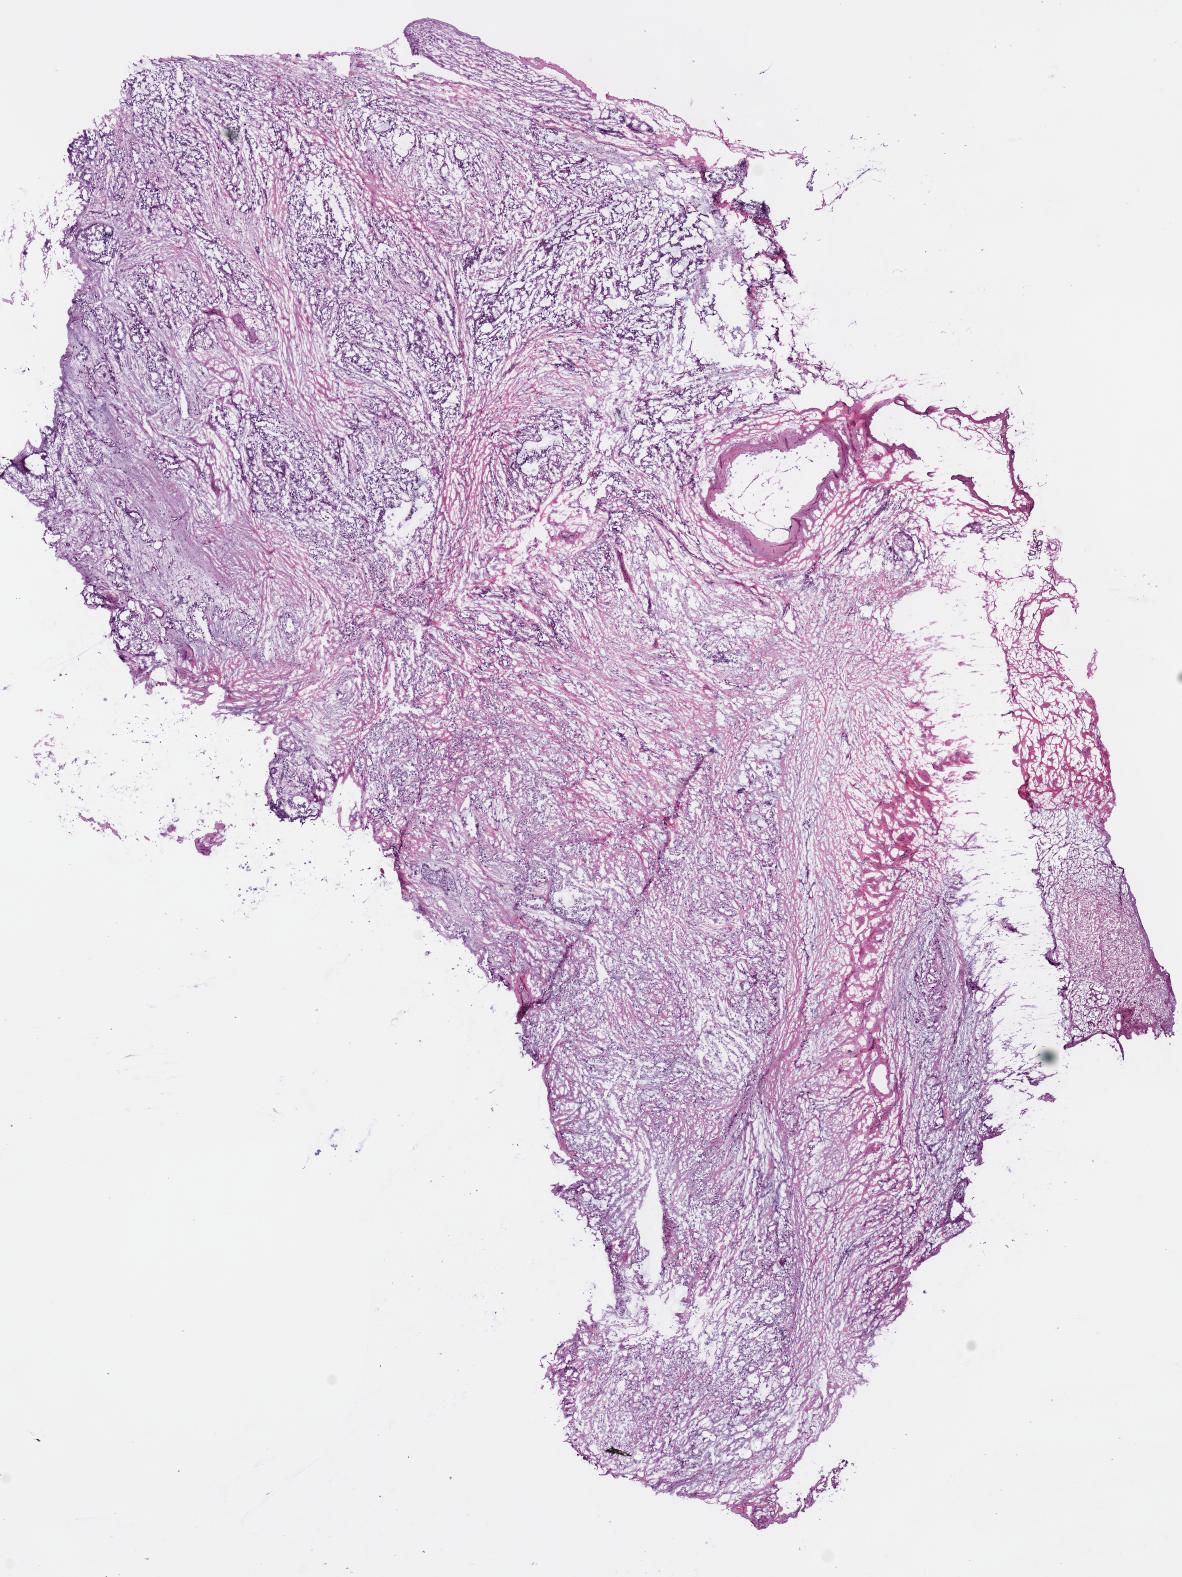
Hematoxylin and eosin (H&E) stained whole-slide image, shown as a low-resolution overview of the whole scanned area (about 9.3 x 12.4 mm, slide scanned at 40x); frozen section; primary tumour sample from the pancreas. Patient: male, age at initial diagnosis 73 years. Histologic grade: G3 (poorly differentiated). Slide review estimates, as recorded: tumour cells 80%, tumour nuclei 85%, normal cells 0%, stromal cells 15%, necrosis 5%.
AJCC pathologic stage: IB (6th edition). Histologic diagnosis: Infiltrating duct carcinoma, NOS.